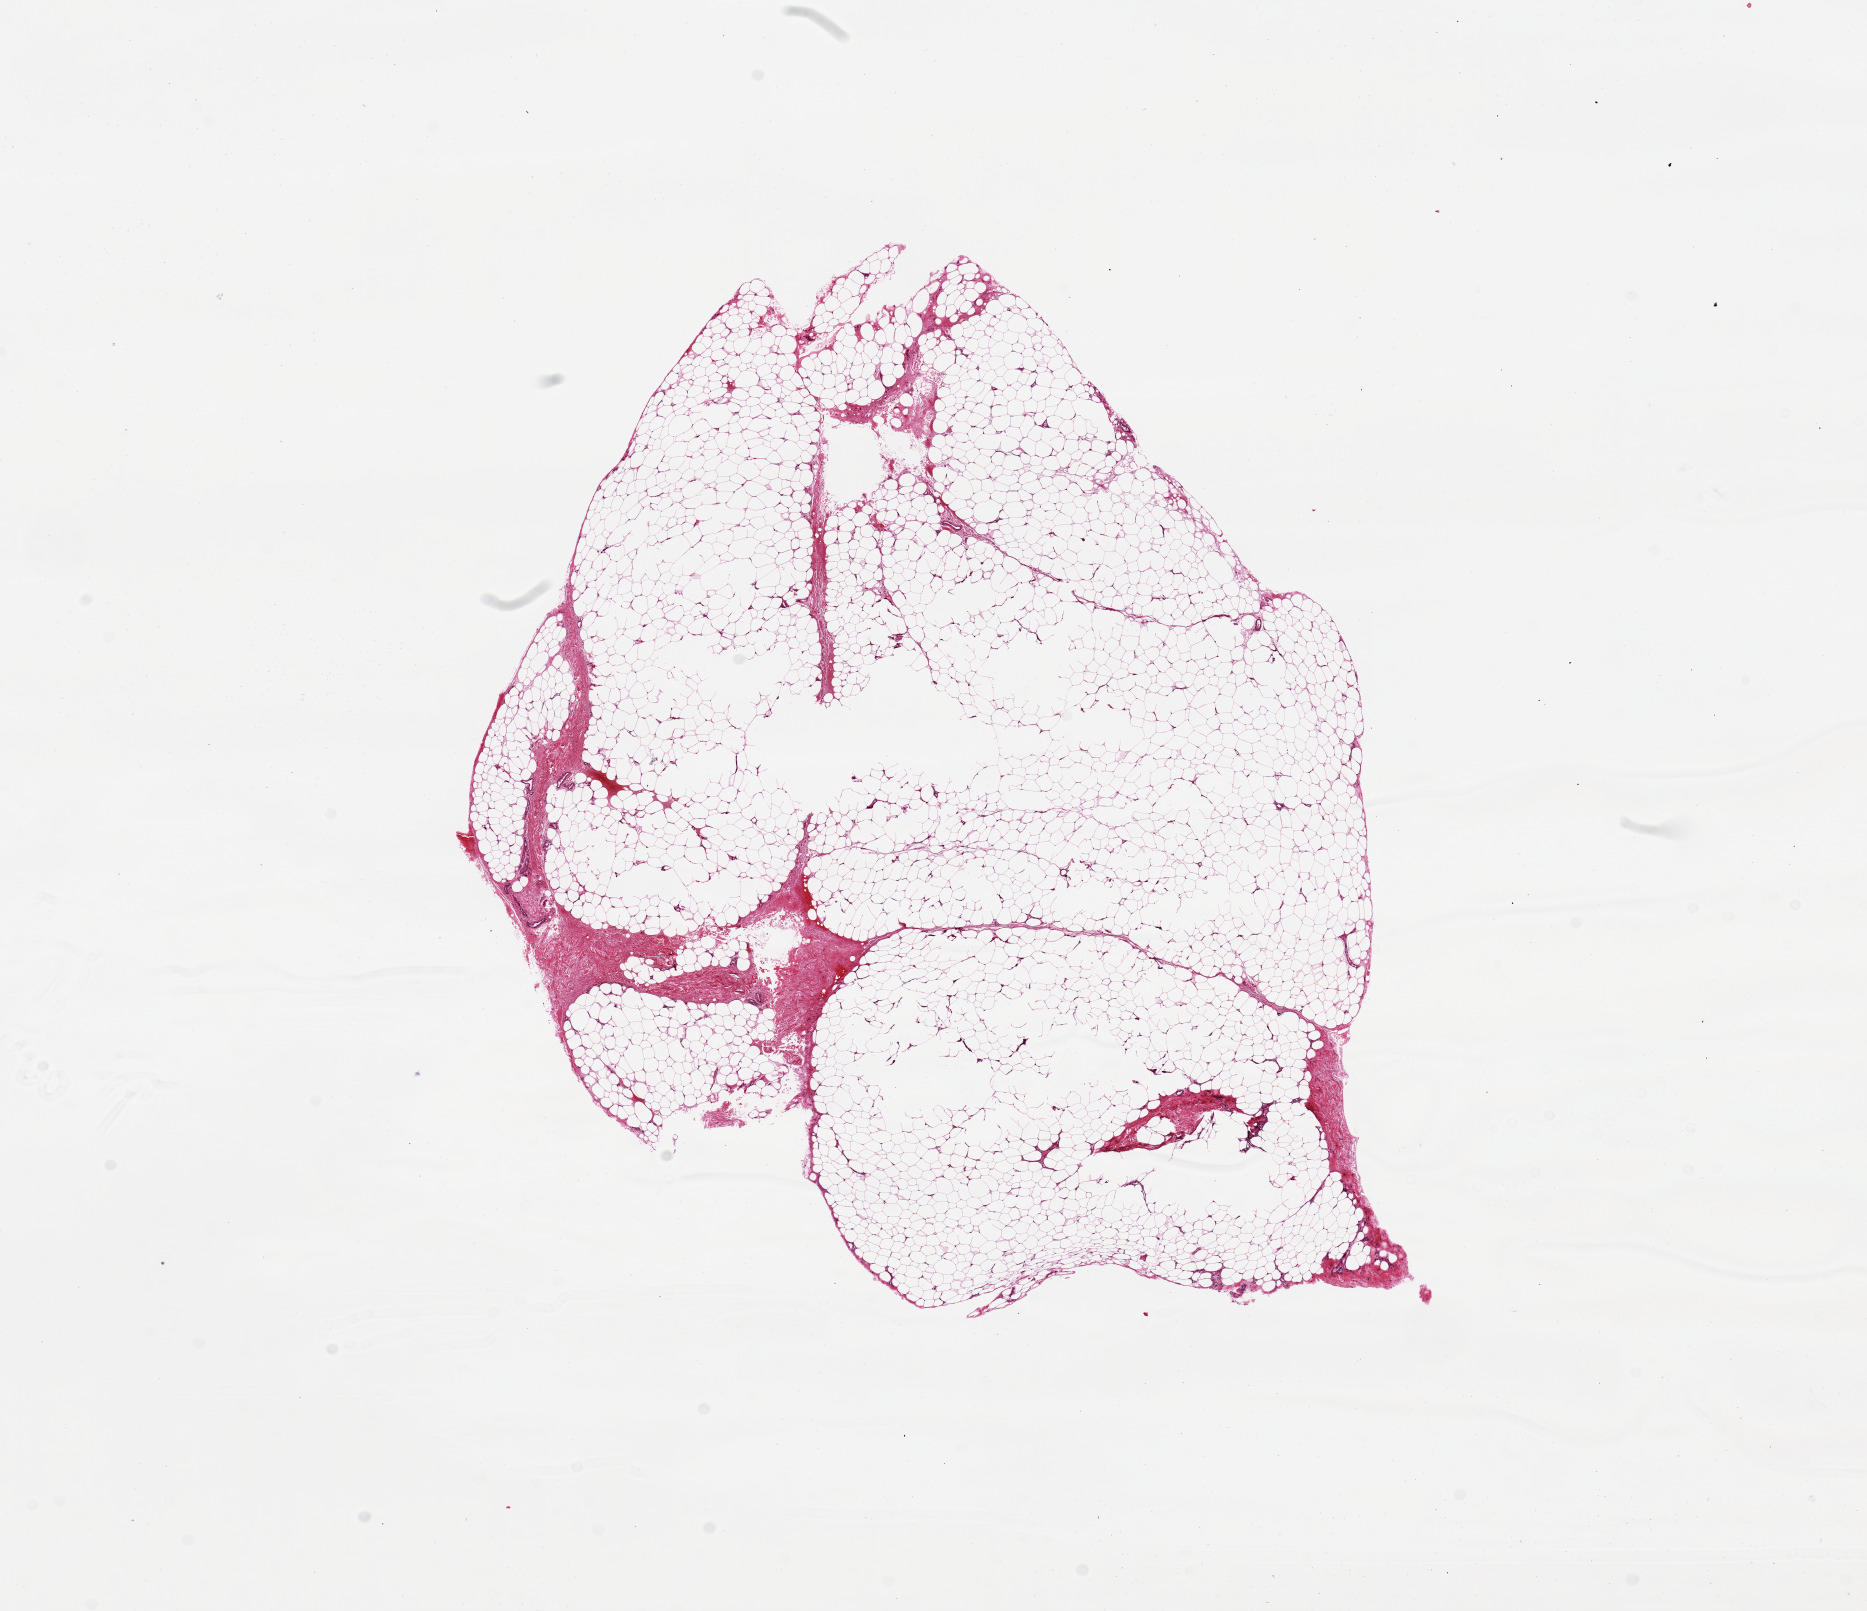
Digitized haematoxylin and eosin-stained section — whole scanned area (about 14.8 x 12.7 mm) shown as a low-resolution overview, PAXgene-fixed, paraffin-embedded tissue, section of adipose tissue (target tissue), donor tissue sample. Donor sex: female.
Reviewer comment on this tissue sample: Artifactual holes.